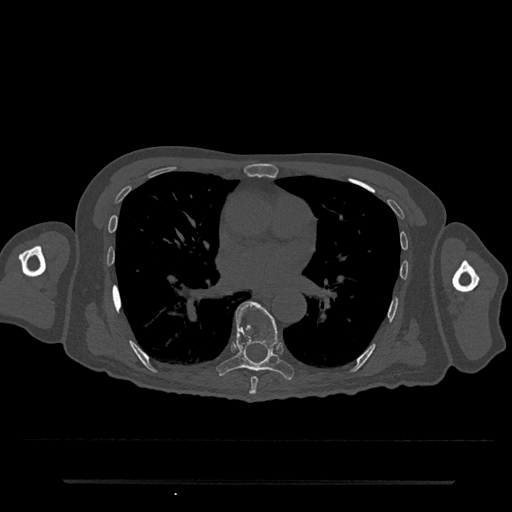
CT including the spine, one axial slice. Position 435 of 797 along the scan axis. 120 kVp. Bone window (W 1800 / L 400 HU). 0.5 mm slice thickness. 512 × 512 image matrix. Patient: male, 74 years. From the clinical record (not read from this slice): primary cancer: prostate.
Annotated regions visible in this slice (semi-automatic segmentation, software-assisted and operator-edited):
- T7 vertebra: box from (x=249, y=377) to (x=258, y=395) px
- T8 vertebra: (x=217, y=301)–(x=294, y=380)